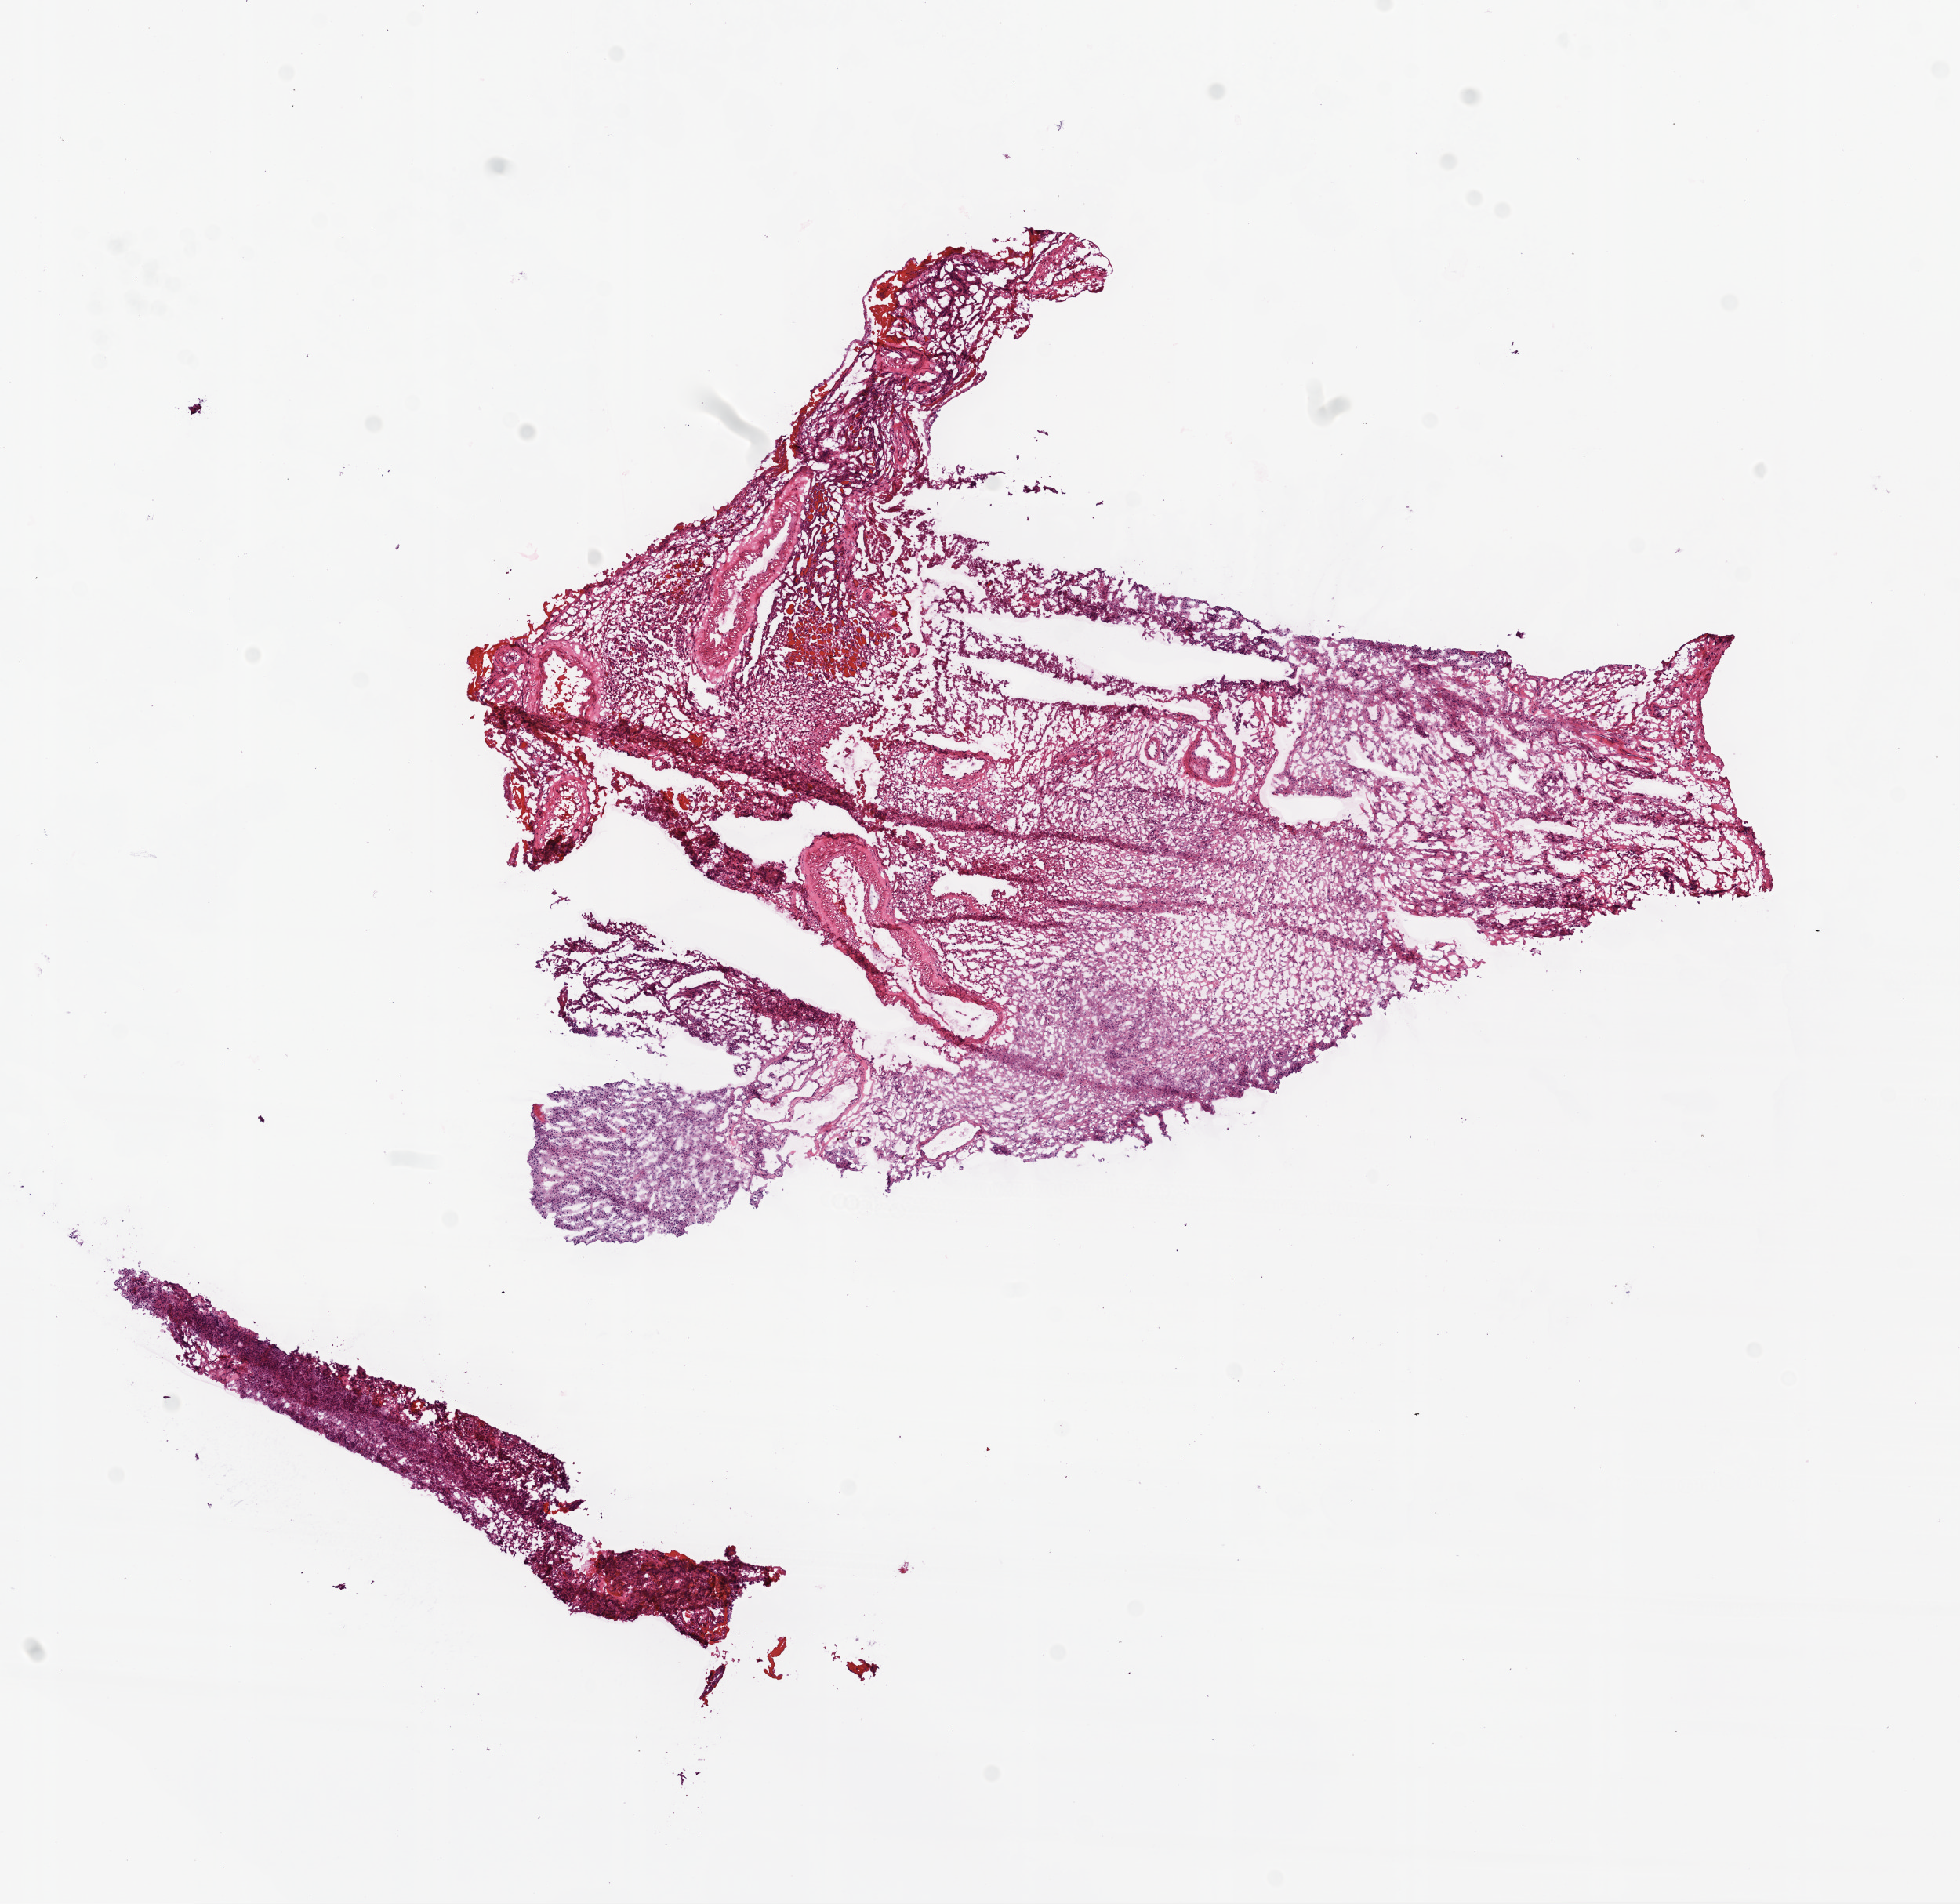
H&E-stained whole-slide image — shown as a low-resolution overview of the whole scanned area (about 10.0 x 9.7 mm); frozen section; sample: primary tumour, brain. Patient: male, age at initial diagnosis 62 years. Slide review estimates, as recorded: tumour cells 80%, tumour nuclei 80%, normal cells 0%, stromal cells 3%, necrosis 17%.
Diagnosis: Glioblastoma.